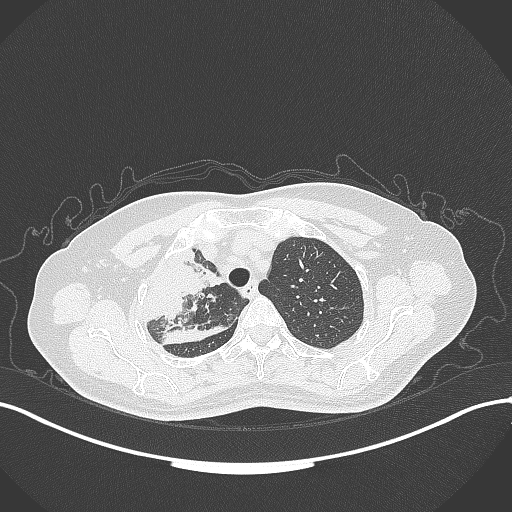
Chest CT, one axial slice. Position 257 of 309 along the scan axis. Reconstruction kernel B70f. 120 kVp. Lung window (W 1500 / L -600 HU). 512 × 512 image matrix. Patient: female, 60 years. Case-level facts recorded for this patient, not image findings: clinical TNM (as recorded): T3 N1 M1.
Outlined on this slice (rectangle marked by the reading radiologist):
- lung tumour (recorded histology: adenocarcinoma): bounding box (x1, y1, x2, y2) in pixels: (132, 243, 231, 328)